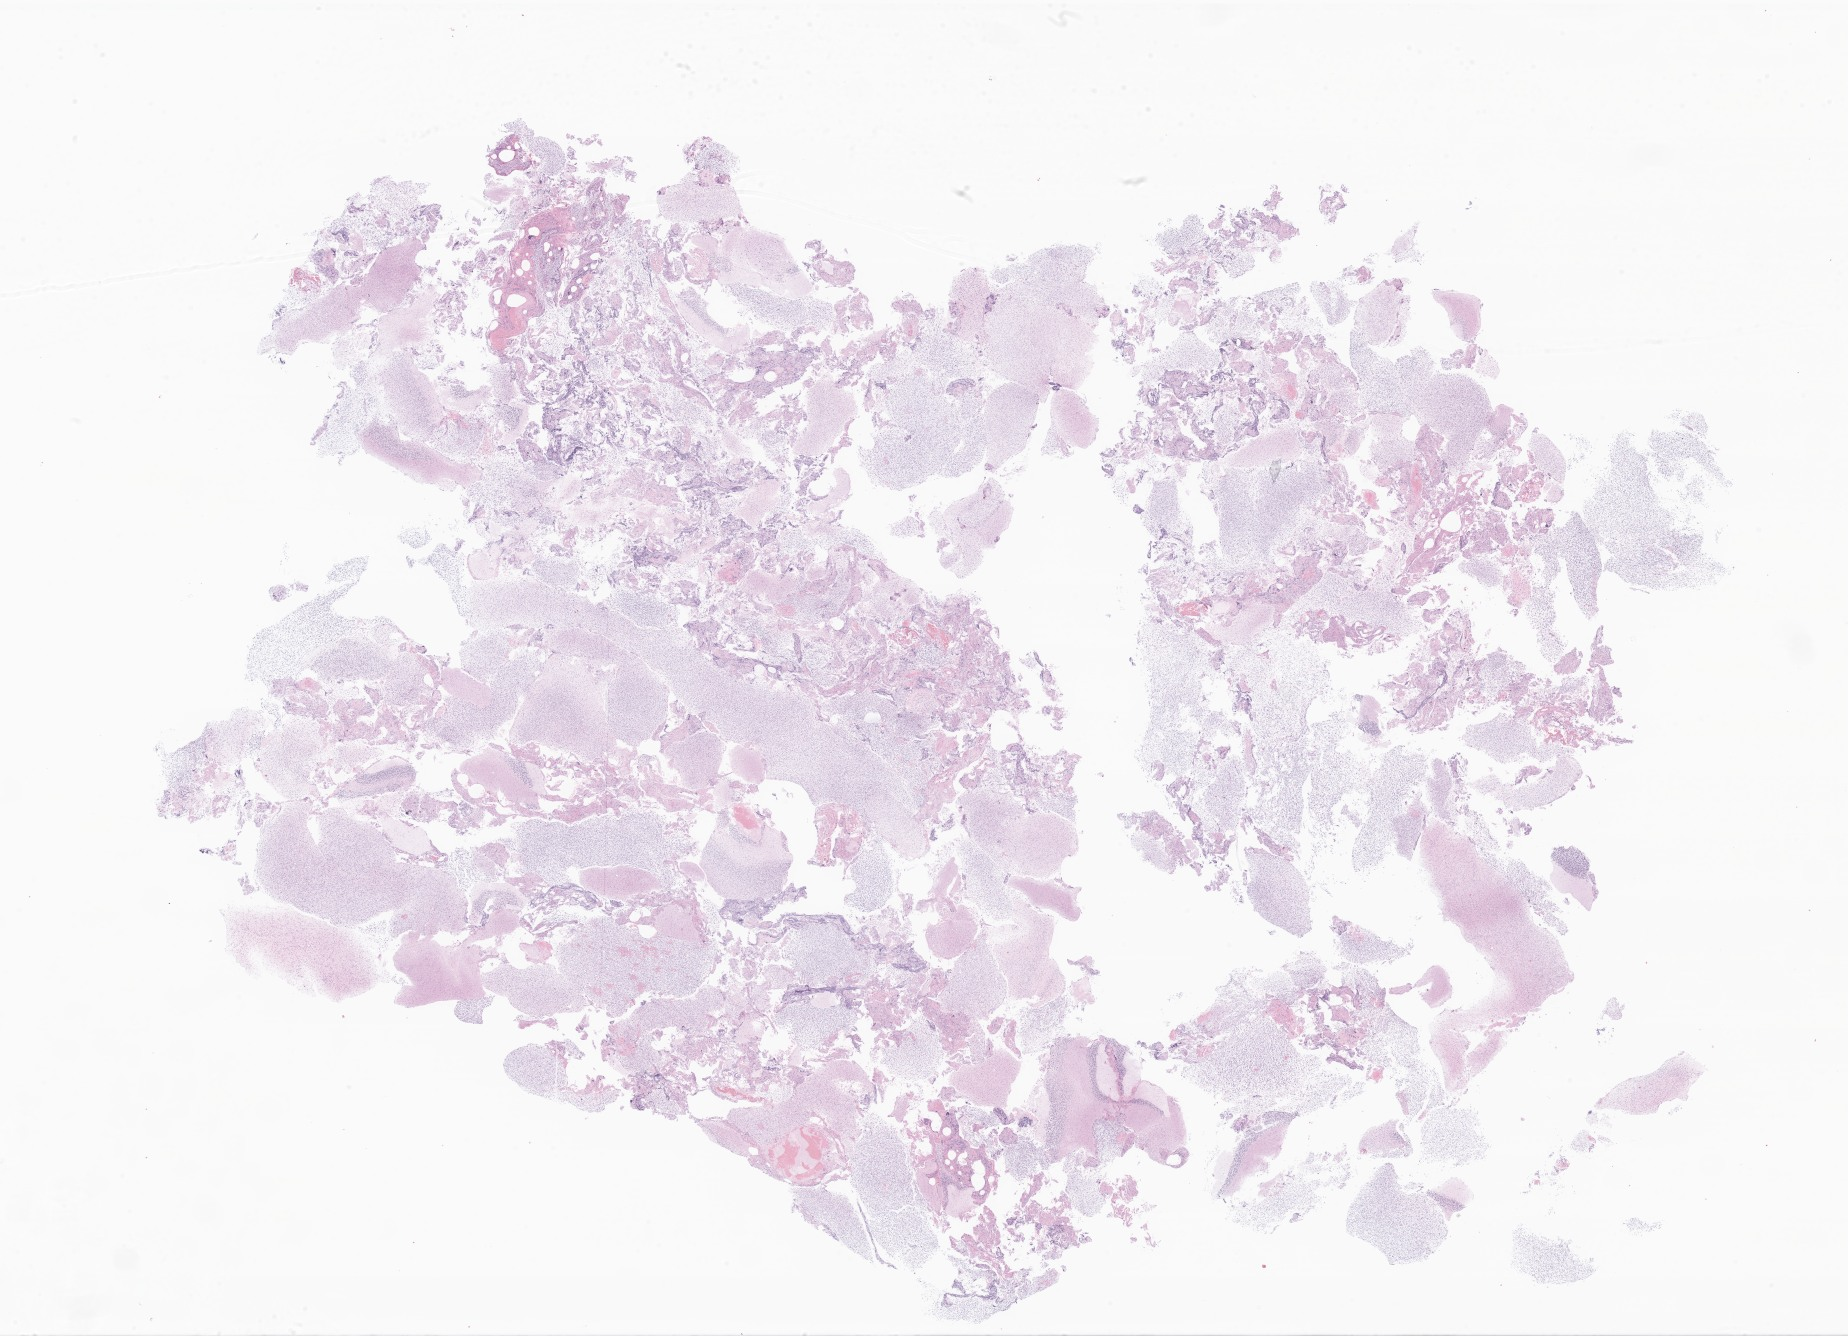
Whole-slide image, H&E stain of tumor tissue from the brain — shown as a low-resolution overview of the whole scanned area (about 31.2 x 22.5 mm), formalin-fixed paraffin-embedded section. Female patient, age 133 months (11 years 1 month).
Diagnosis: Glioma, malignant.